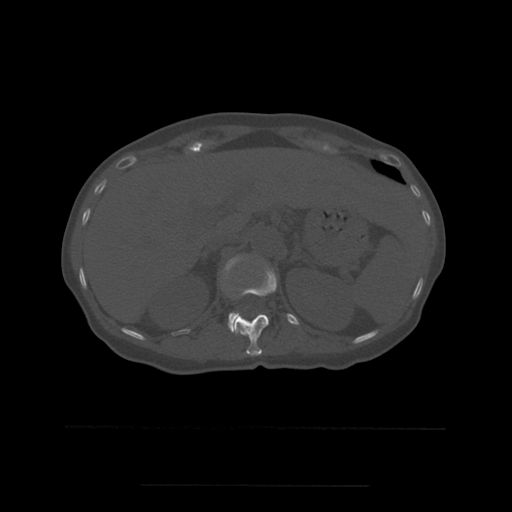
CT including the spine, one axial slice; slice 250 of 544 in the series (ordered by position); bone window (W 1800 / L 400 HU); 512 × 512 image matrix. Patient age 58 years. From the clinical record (not read from this slice): primary cancer: lung.
Annotated regions visible in this slice (semi-automatically segmented with operator editing):
- L1 vertebra: bounding box <225,257,269,332> (left, top, right, bottom; pixels)
- T12 vertebra: <232,267,277,356>